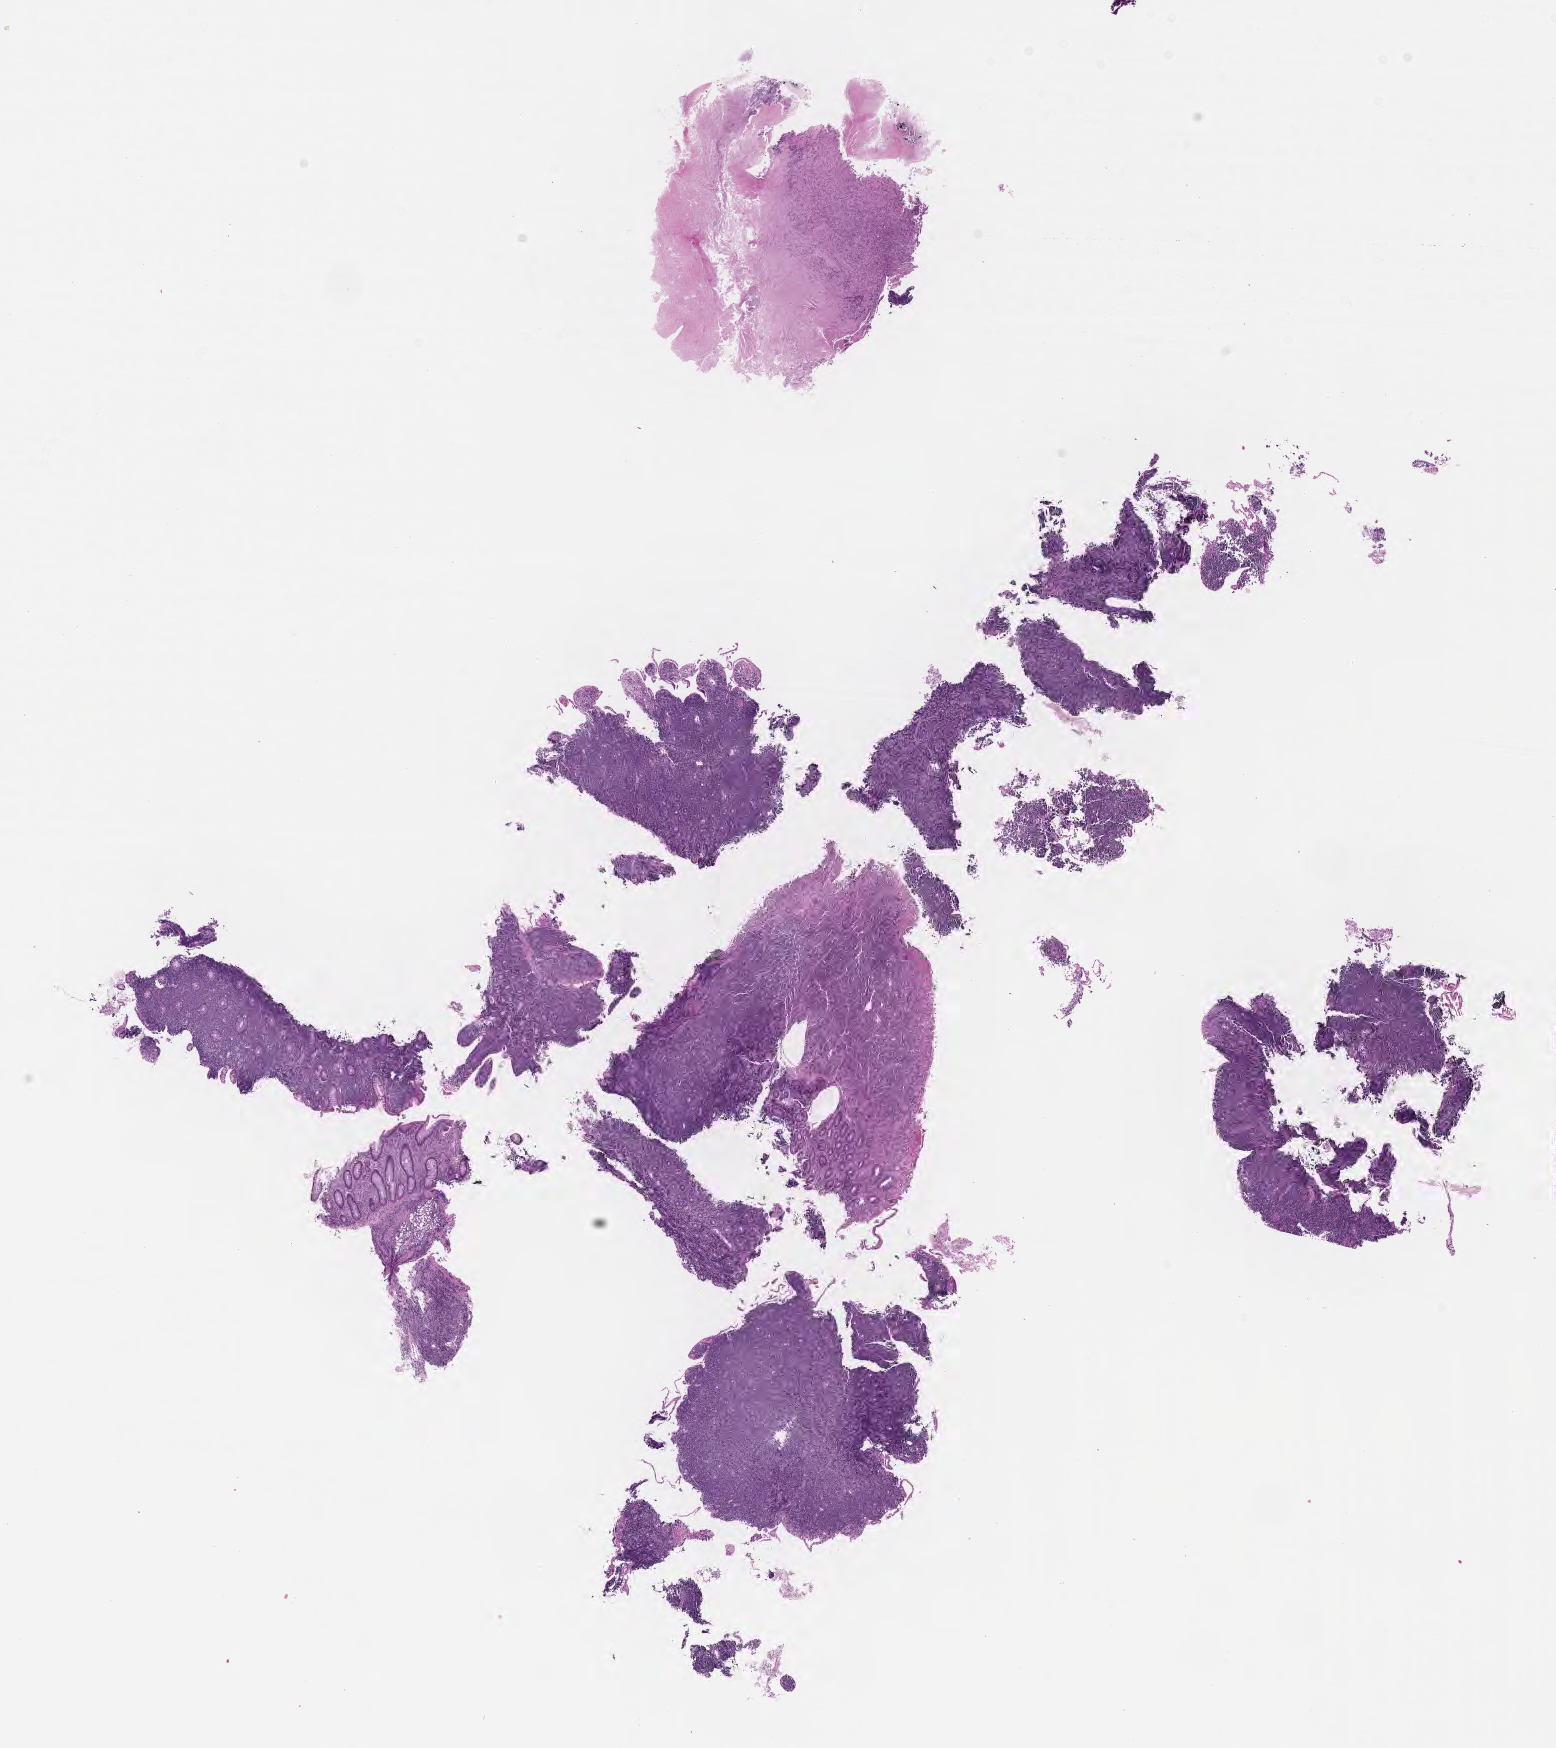
Digitized haematoxylin and eosin-stained section — shown as a low-resolution overview of the whole scanned area (about 12.6 x 14.1 mm), formalin-fixed paraffin-embedded section, specimen: primary tumor. Patient: male, aged 56. Slide review estimates, as recorded: tumor cells 55%, tumor nuclei 85%, stromal cells 5%, necrosis 30%, normal cells 10%. Infiltration values recorded for this section: lymphocyte infiltration 35%, monocyte infiltration 20%, neutrophil infiltration 20%.
Histologic diagnosis: Burkitt lymphoma, NOS. Section: top of the tissue portion. Ann Arbor stage (patient): Stage IV.